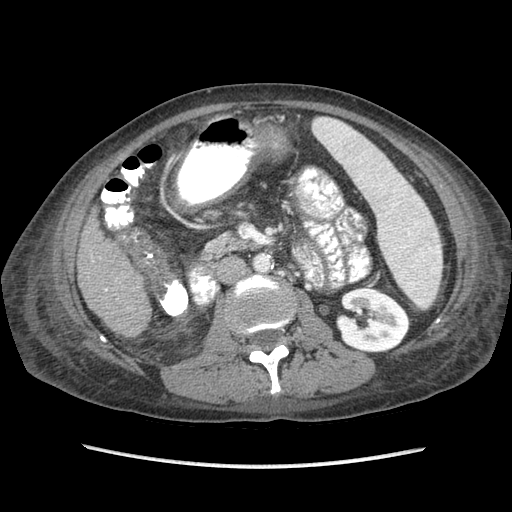
Contrast-enhanced abdominal CT (liver protocol), one axial slice. Position 24 of 87 along the scan axis. Reconstruction kernel STANDARD. 120 kVp. Soft-tissue window (W 400 / L 40 HU). 2.5 mm slice thickness. 512 × 512 image matrix, field of view 340 × 340 mm. From the clinical record (not read from this slice): diagnosis: hepatocellular carcinoma (patient treated with transarterial chemoembolisation; whether this scan precedes or follows treatment is not stated here); TNM stage (as recorded): Stage-IIIB; Child-Pugh class: A; tumour differentiation: no biopsy.
Outlined on this slice (semi-automatic segmentation, software-assisted and operator-edited):
- liver parenchyma outside the tumour (the mass and vessels are separate outlines, so this box may not span the whole liver): bounding box (x1, y1, x2, y2) in pixels: (78, 208, 150, 335)
- liver vessels: (105, 289, 108, 291)